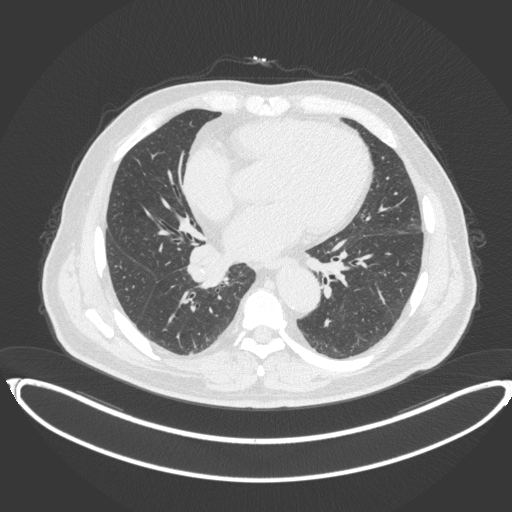
Chest CT, one axial slice; slice 183 of 383 in the series (ordered by position); reconstruction kernel B31f; 120 kVp; lung window (W 1500 / L -600 HU); 1 mm slice thickness; 512 × 512 image matrix. Patient: male, 61 years. Case-level facts recorded for this patient, not image findings: clinical TNM (as recorded): T1b N1 M0.
Outlined on this slice (rectangle marked by the reading radiologist):
- lung tumour (recorded histology: squamous cell carcinoma): bounding box (x1, y1, x2, y2) in pixels: (185, 243, 228, 289)